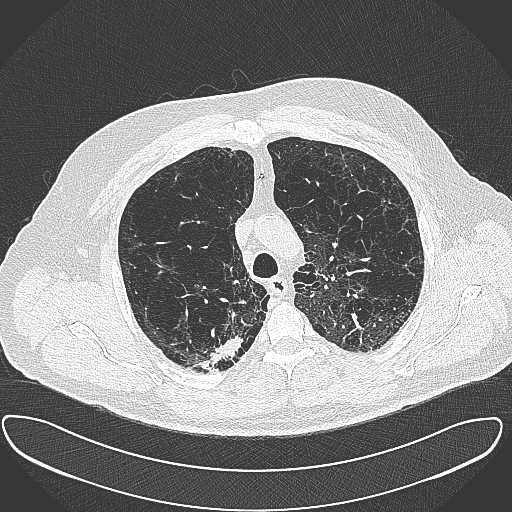
Chest CT (low-dose screening protocol), one axial image, baseline annual screen, lung window (W 1500 / L -600 HU), lung (sharp) reconstruction kernel (B80f), 512 × 512 image matrix, field of view 408 × 408 mm. Male participant, aged 60 years at enrolment. Current smoker at enrolment.
Lesion marked by an expert reader, bounding box (x1, y1, x2, y2) in pixels: (194, 327, 248, 375). The exam's reader record, not a measurement of the box and not confirmed to be the same lesion: non-calcified nodule or mass ≥4 mm, right upper lobe, 15 × 25 mm, spiculated (stellate) margins, soft tissue attenuation. Later outcome: lung cancer diagnosed 32 days after this screen — carcinoma, NOS, right upper lobe, moderately differentiated (G2), stage IB (AJCC 6th edition), 35 mm at pathology.